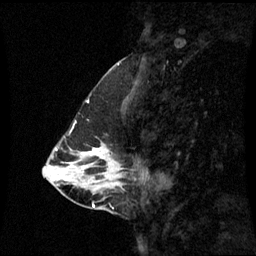
Breast MRI (dynamic contrast-enhanced), one sagittal slice; slice 25 of 60 in the series (ordered by position); dynamic contrast-enhanced series, image 2 of 3 at this slice position (ordered by acquisition); 1.5 T; TE 4.2 ms, TR 8.9 ms; 256 × 256 image matrix, field of view 240 × 240 mm. Patient: female, 43 years. From the clinical record (not read from this slice): setting: breast cancer imaged before/during neoadjuvant chemotherapy; receptor status: HR-positive, HER2-negative.
Annotated regions visible in this slice (semi-automatic segmentation, software-assisted and operator-edited):
- analysis volume of interest (the breast-tissue region the enhancement analysis was run in; not a lesion): box from (x=78, y=144) to (x=124, y=193) px
- tumour enhancement mask (voxels above the 70 % enhancement threshold inside the analysis volume of interest): (x=90, y=148)–(x=99, y=155)